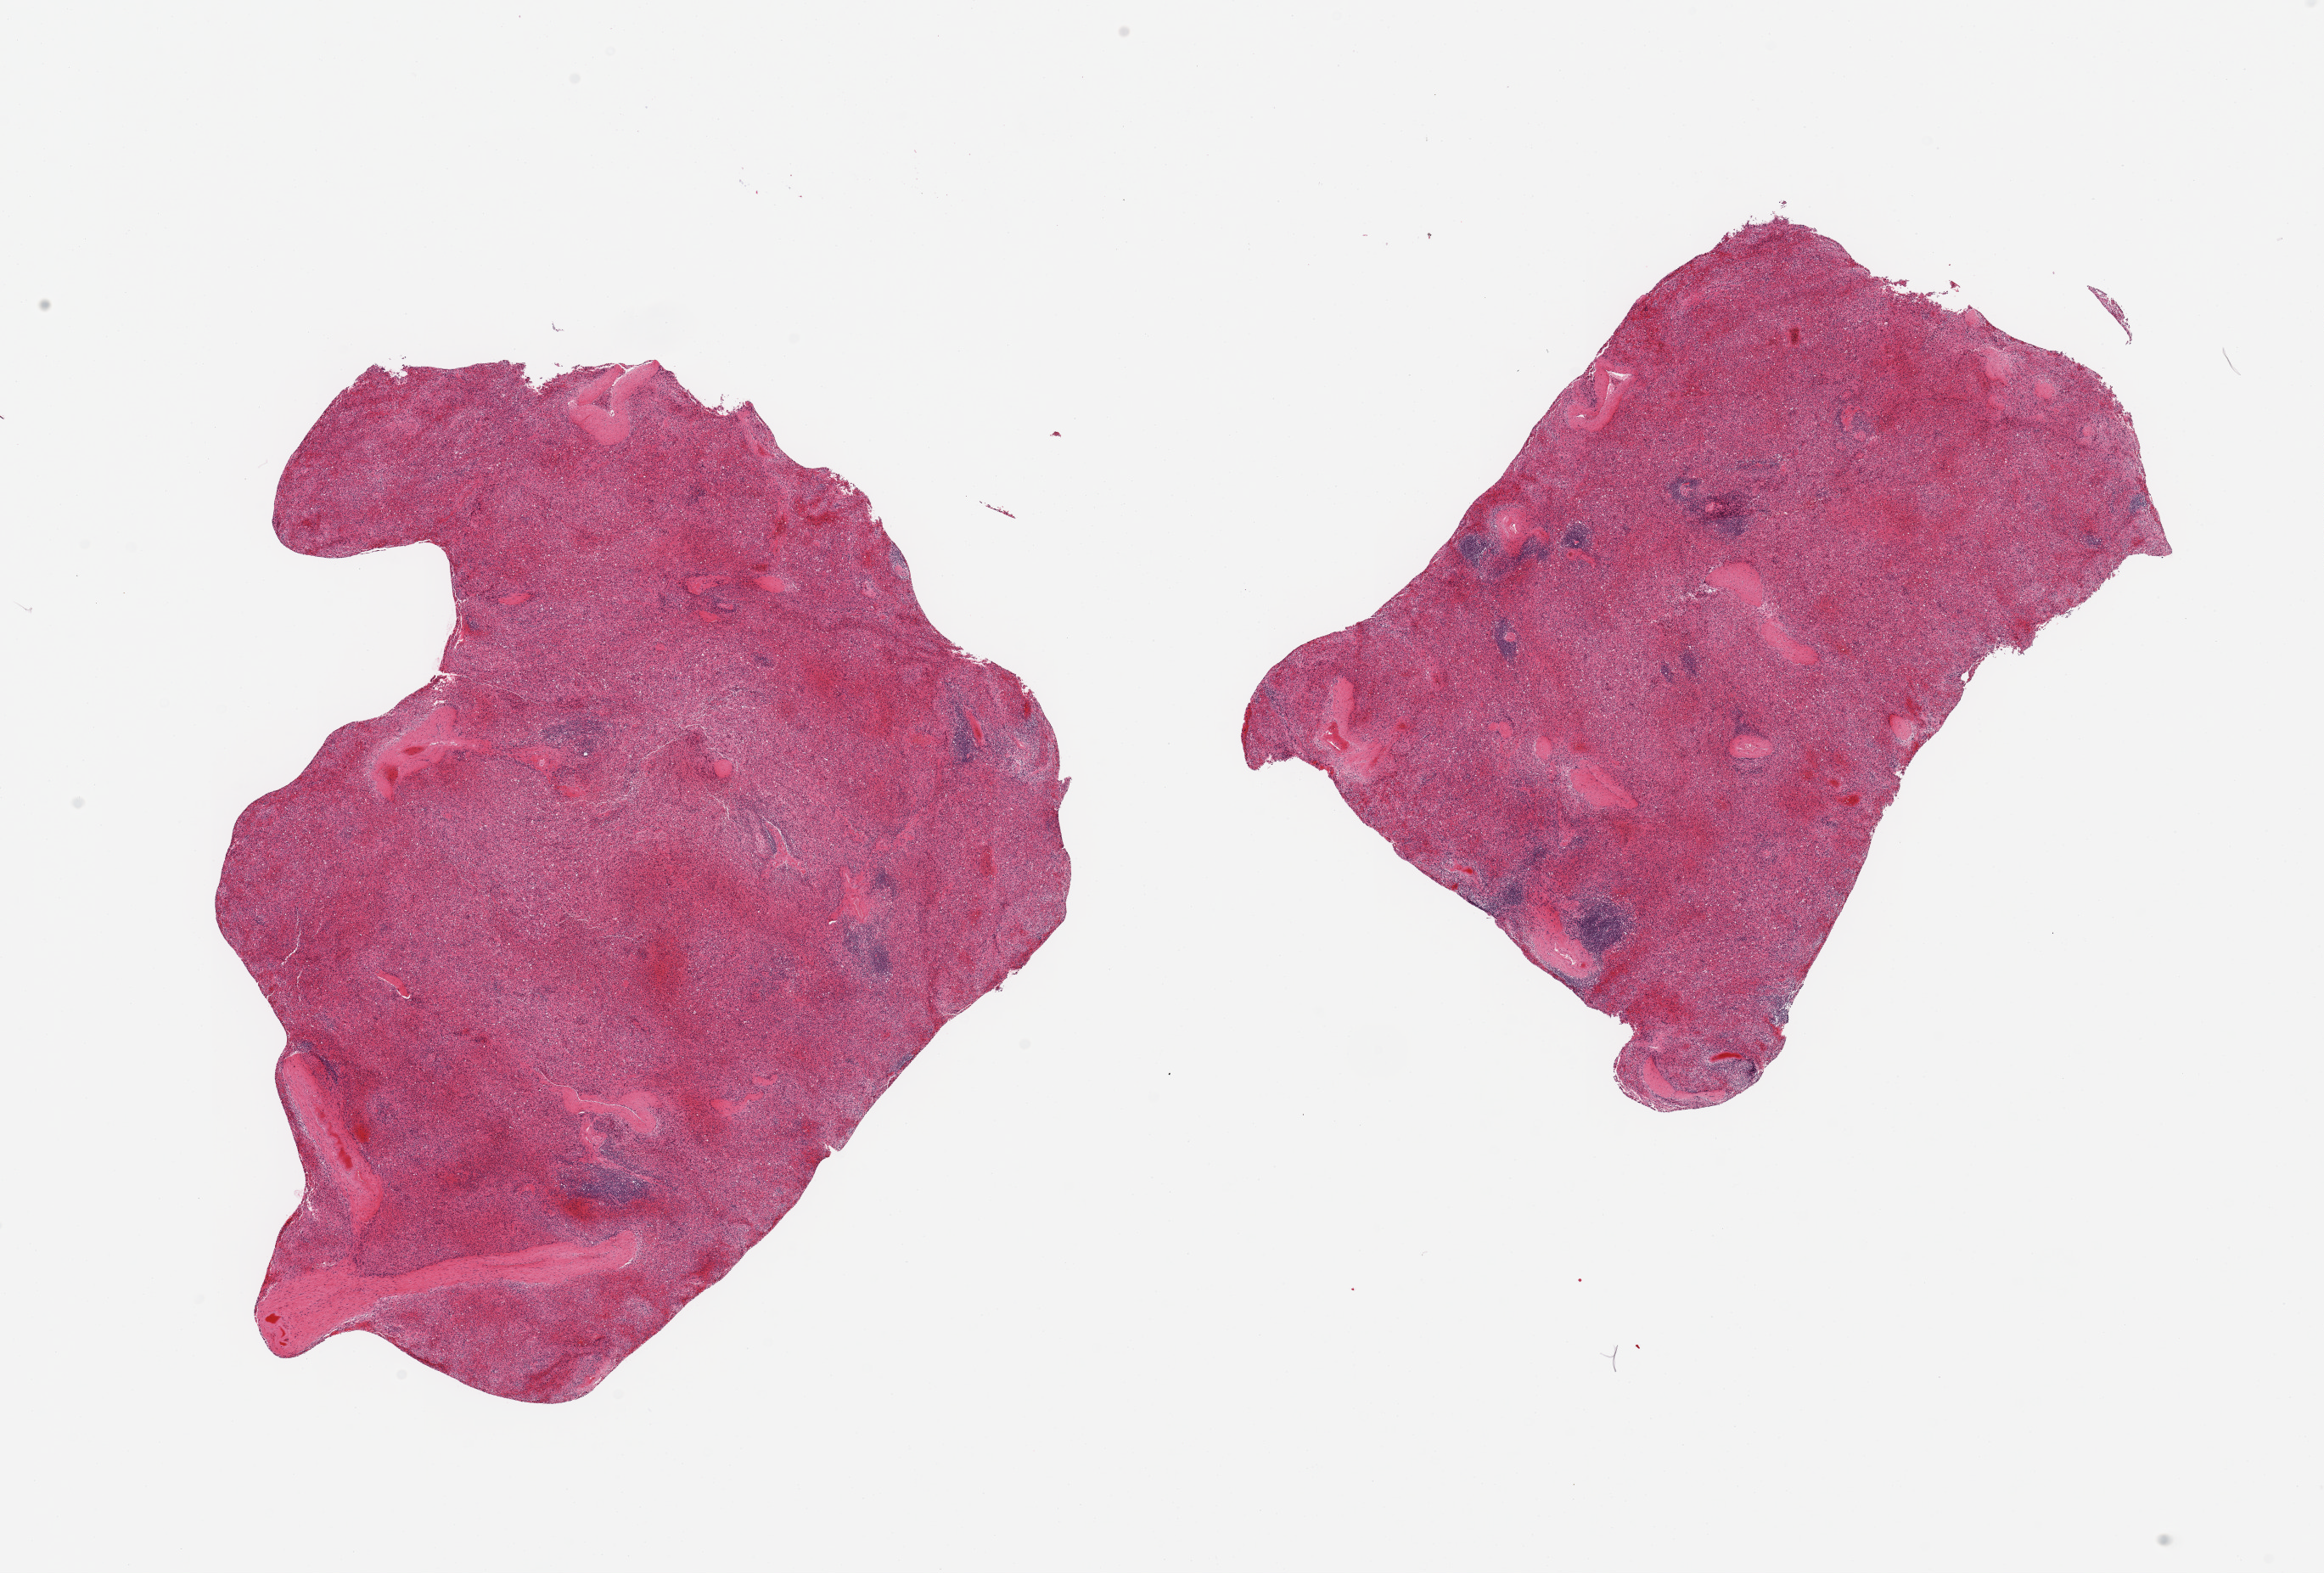
Hematoxylin and eosin (H&E) whole-slide image, brightfield — a low-resolution overview of the entire scanned area, about 21.7 x 14.7 mm (slide scanned at 20x); PAXgene-fixed, paraffin-embedded tissue; section of spleen (target tissue); donor tissue sample. Donor sex: female.
* reviewer comment on this tissue sample: 2 pieces; some congestion